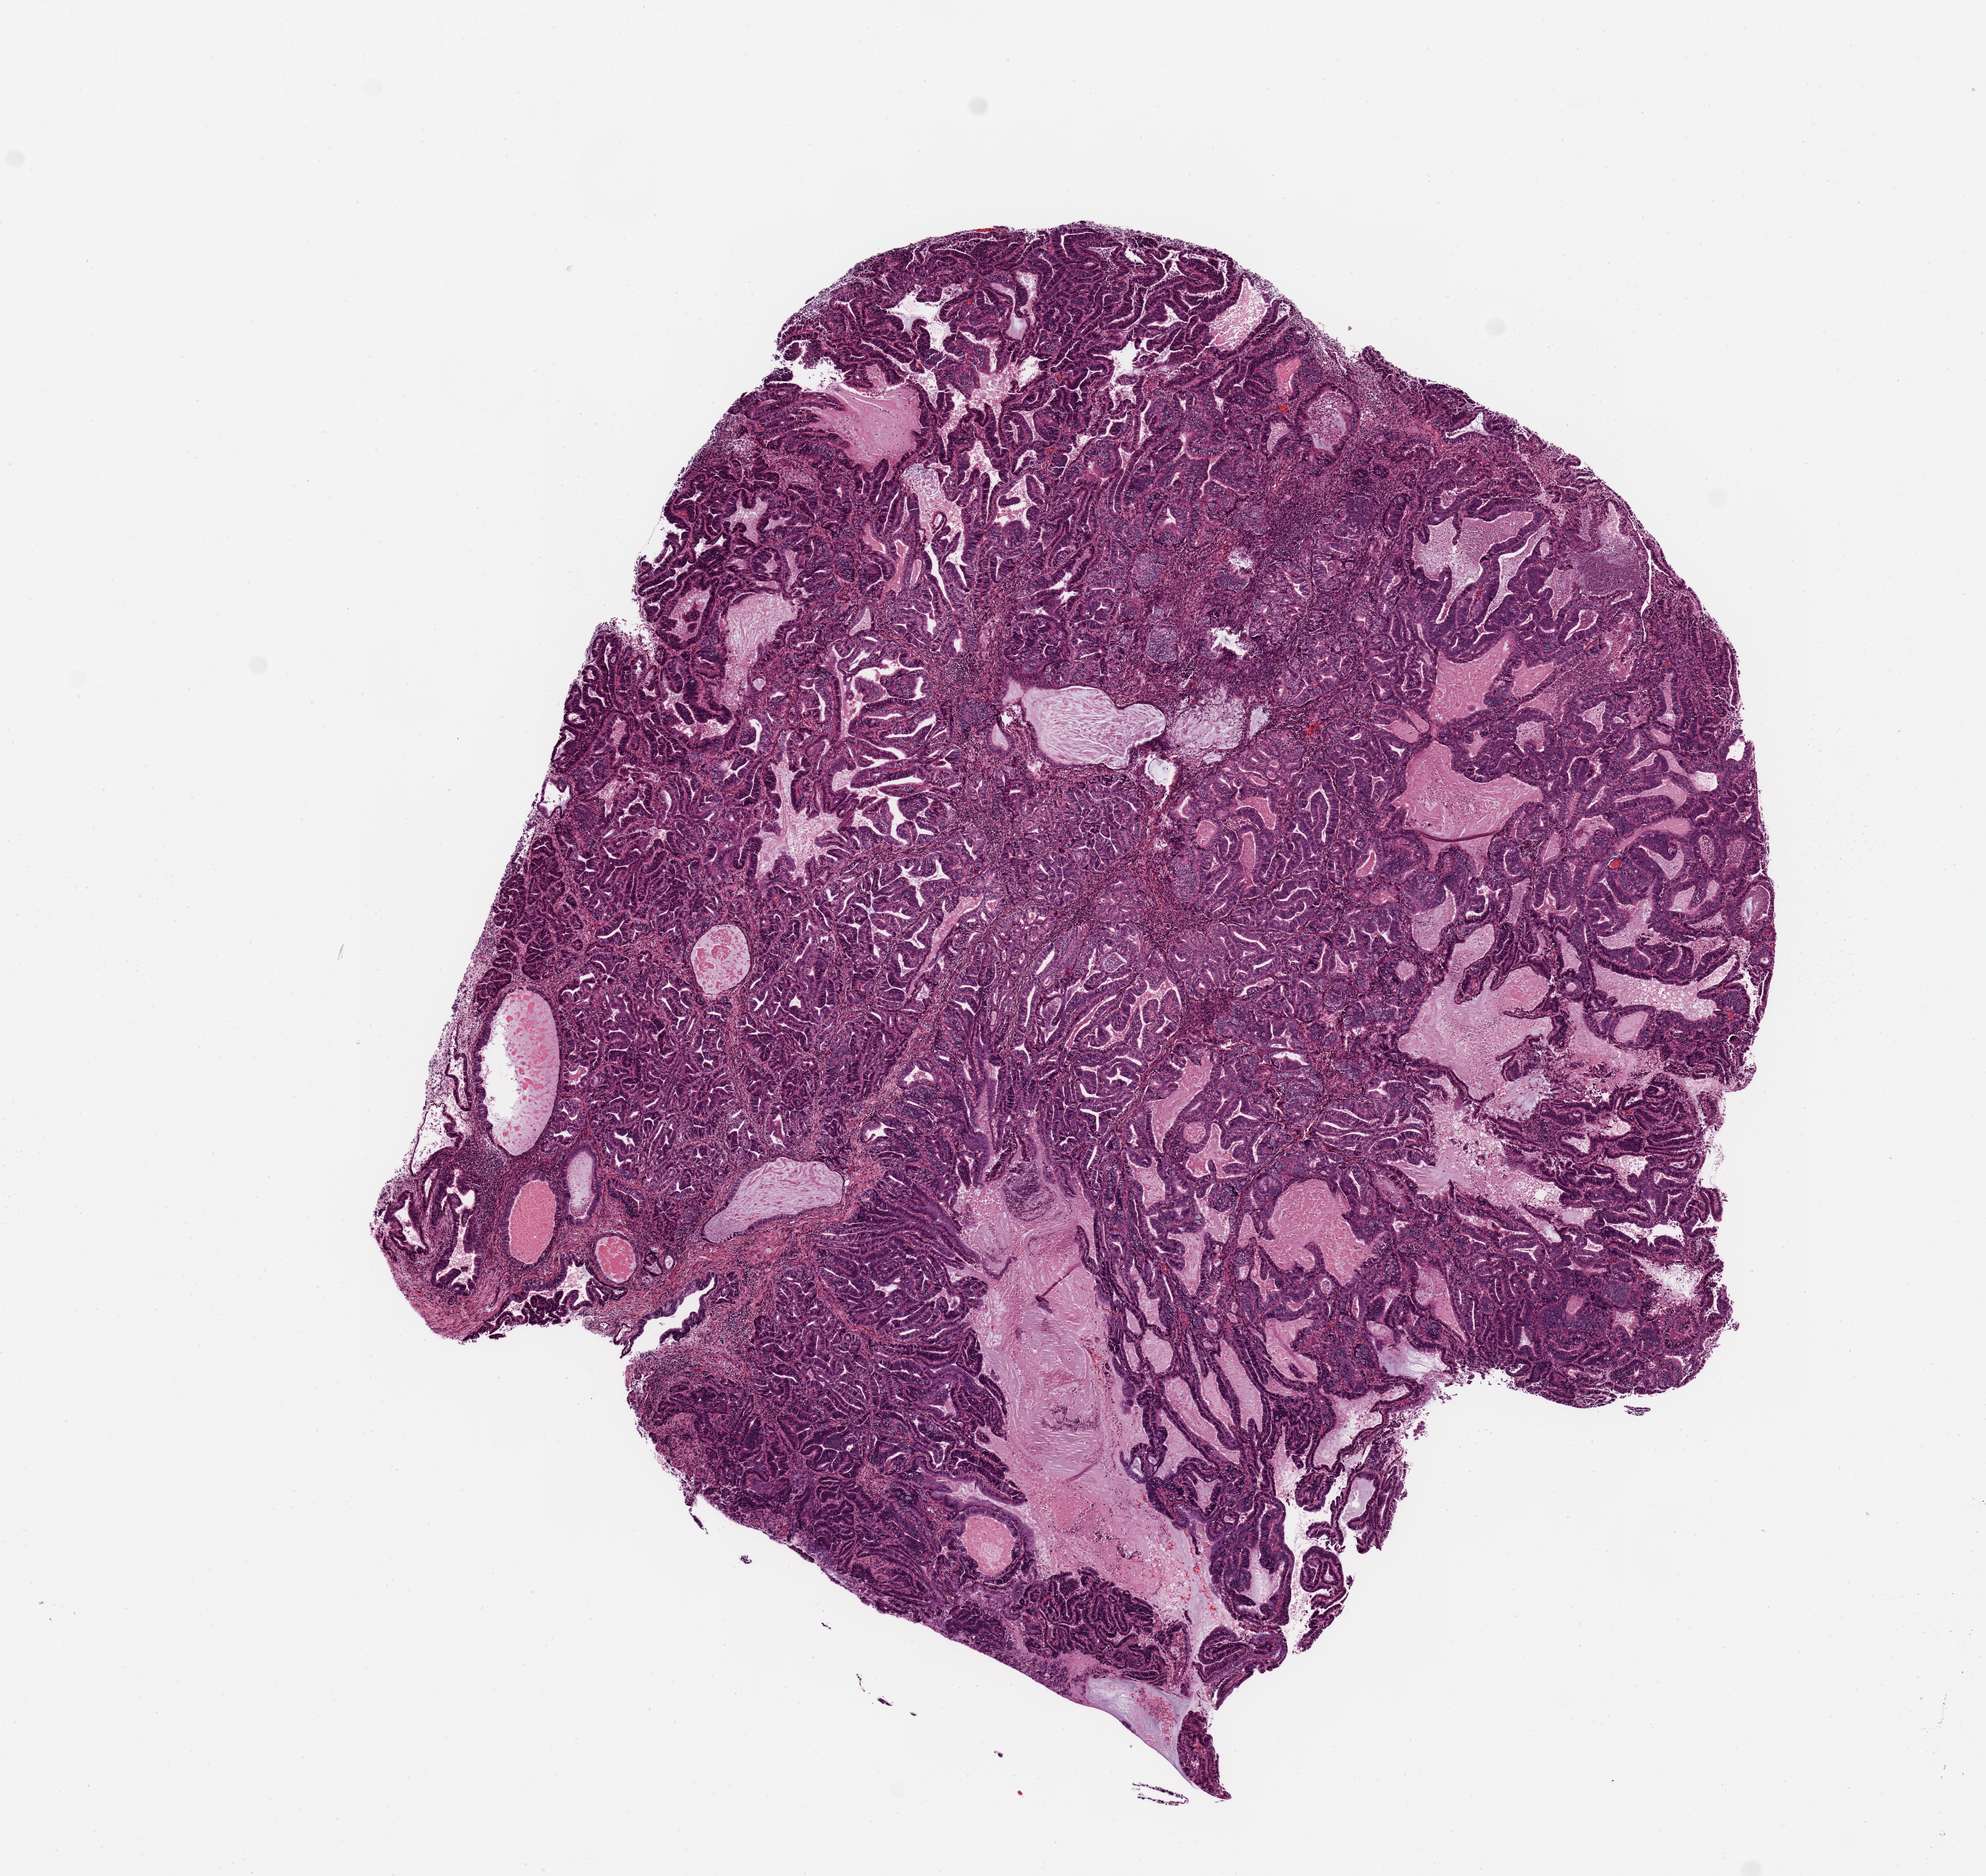
Hematoxylin and eosin (H&E) stained whole-slide image — shown as a low-resolution overview of the whole scanned area (about 10.8 x 10.2 mm, slide scanned at 20x); tumour tissue sample, uterus. 64-year-old female patient. Histologic grade: G1 (well differentiated).
* primary tumour site (as recorded): anterior endometrium
* diagnosis: Endometrioid adenocarcinoma, NOS
* AJCC pathologic stage: I